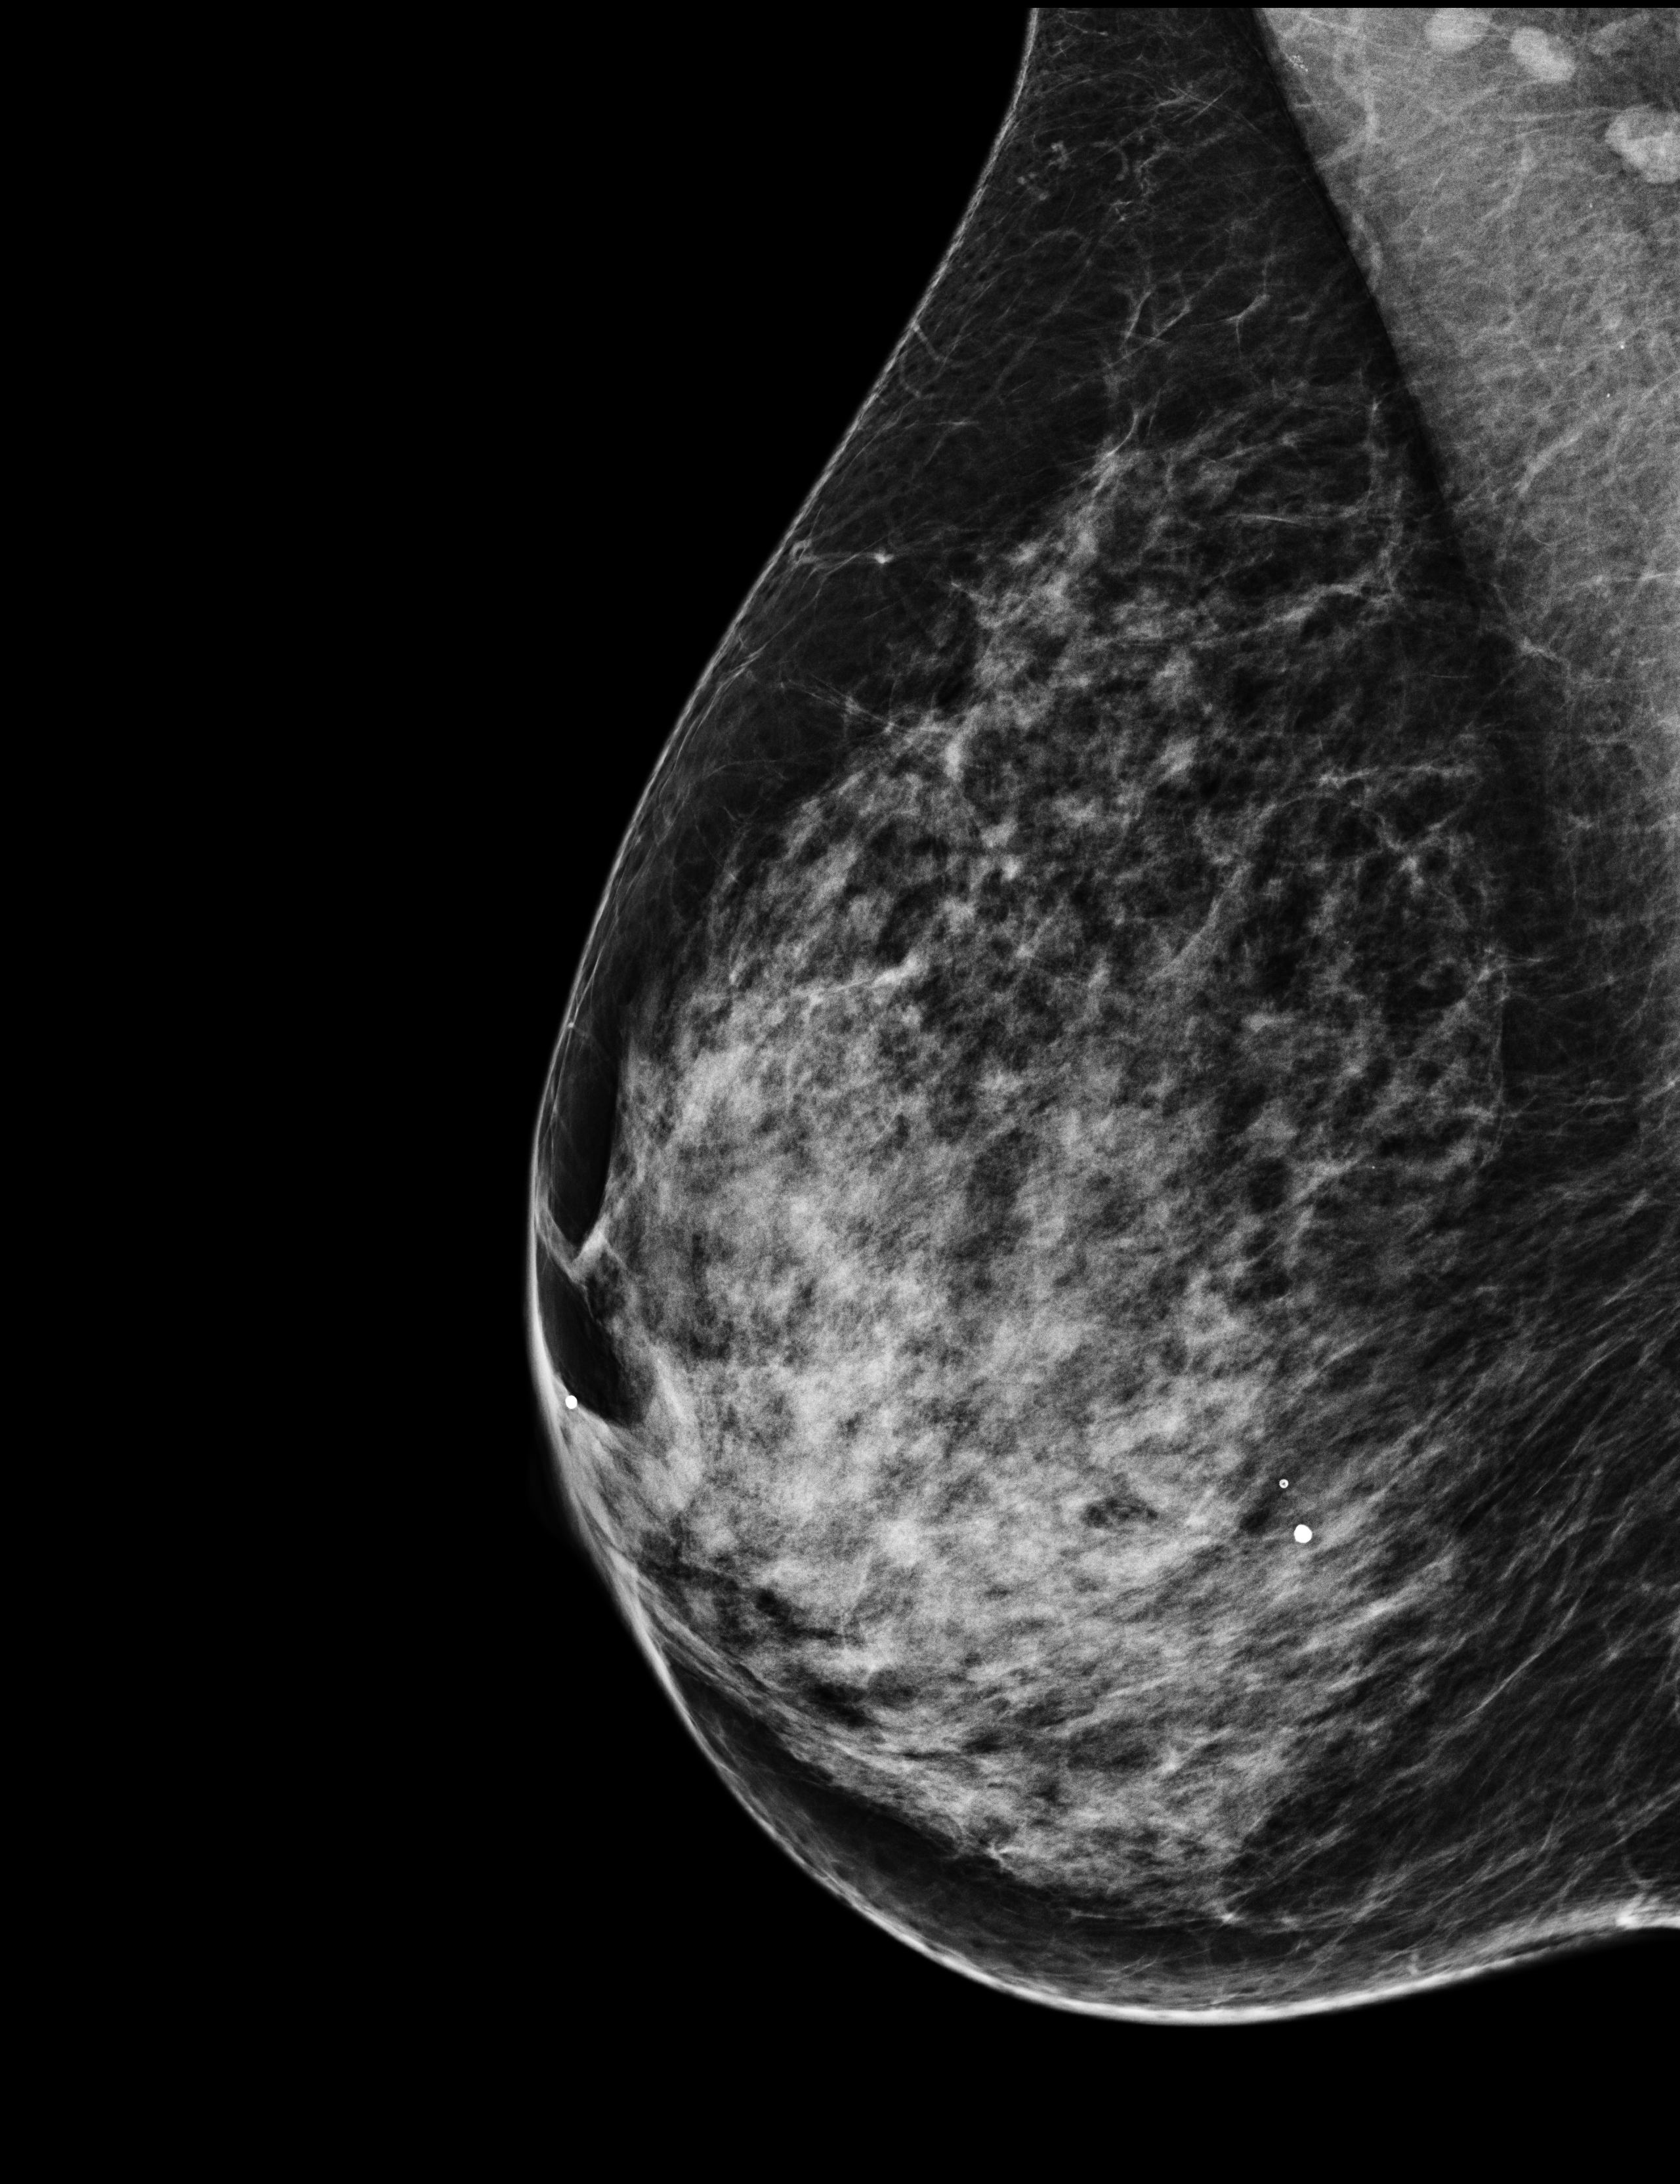
Annual screening mammography examination, compressed breast thickness 54 mm. Patient: female, 59 years.
Image type: full-field digital mammogram. Breast: right. Projection: medio-lateral oblique projection.